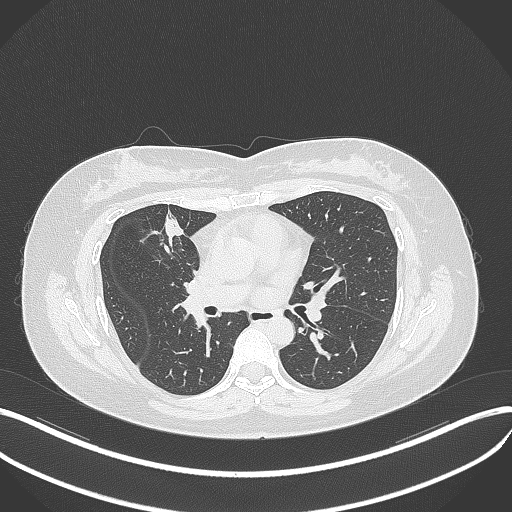
Chest CT, one axial slice. Position 171 of 273 along the scan axis. 120 kVp. Lung window (W 1500 / L -600 HU). 512 × 512 image matrix, field of view 400 × 400 mm. Patient: female, 42 years. From the clinical record (not read from this slice): clinical TNM (as recorded): T1b N0 M0.
Structures marked on this image (rectangle marked by the reading radiologist):
- lung tumour (recorded histology: adenocarcinoma): bounding box (x1, y1, x2, y2) in pixels: (155, 207, 183, 250)